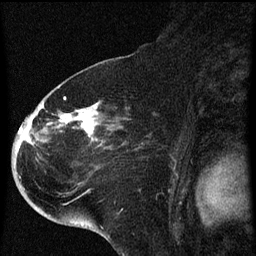
Breast MRI (dynamic contrast-enhanced), one sagittal slice. Slice 36 of 60 in the series (ordered by position). Dynamic contrast-enhanced series, image 2 of 4 at this slice position (ordered by acquisition). 1.5 T. TE 4.2 ms, TR 8 ms. 2 mm slice thickness. 256 × 256 image matrix. Patient: female, 71 years.
Annotated regions visible in this slice (semi-automatic segmentation, software-assisted and operator-edited):
- analysis volume of interest (the breast-tissue region the enhancement analysis was run in; not a lesion): bounding box (x1, y1, x2, y2) in pixels: (32, 86, 141, 205)
- tumour enhancement mask (voxels above the 70 % enhancement threshold inside the analysis volume of interest): (41, 98, 98, 141)